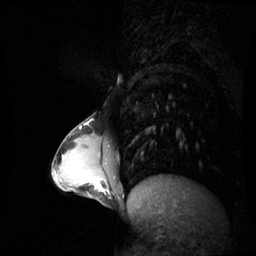
Breast MRI (dynamic contrast-enhanced), one sagittal slice. Dynamic contrast-enhanced series, image 2 of 3 at this slice position (ordered by acquisition). 1.5 T. TE 4.2 ms, TR 8.9 ms. 256 × 256 image matrix. Patient: female, 34 years. Case-level facts recorded for this patient, not image findings: setting: breast cancer imaged before/during neoadjuvant chemotherapy; receptor status: triple-negative.
Annotated regions visible in this slice (semi-automatic segmentation, software-assisted and operator-edited):
- analysis volume of interest (the breast-tissue region the enhancement analysis was run in; not a lesion): bounding box (x1, y1, x2, y2) in pixels: (65, 168, 108, 200)
- tumour enhancement mask (voxels above the 70 % enhancement threshold inside the analysis volume of interest): (93, 180, 104, 191)